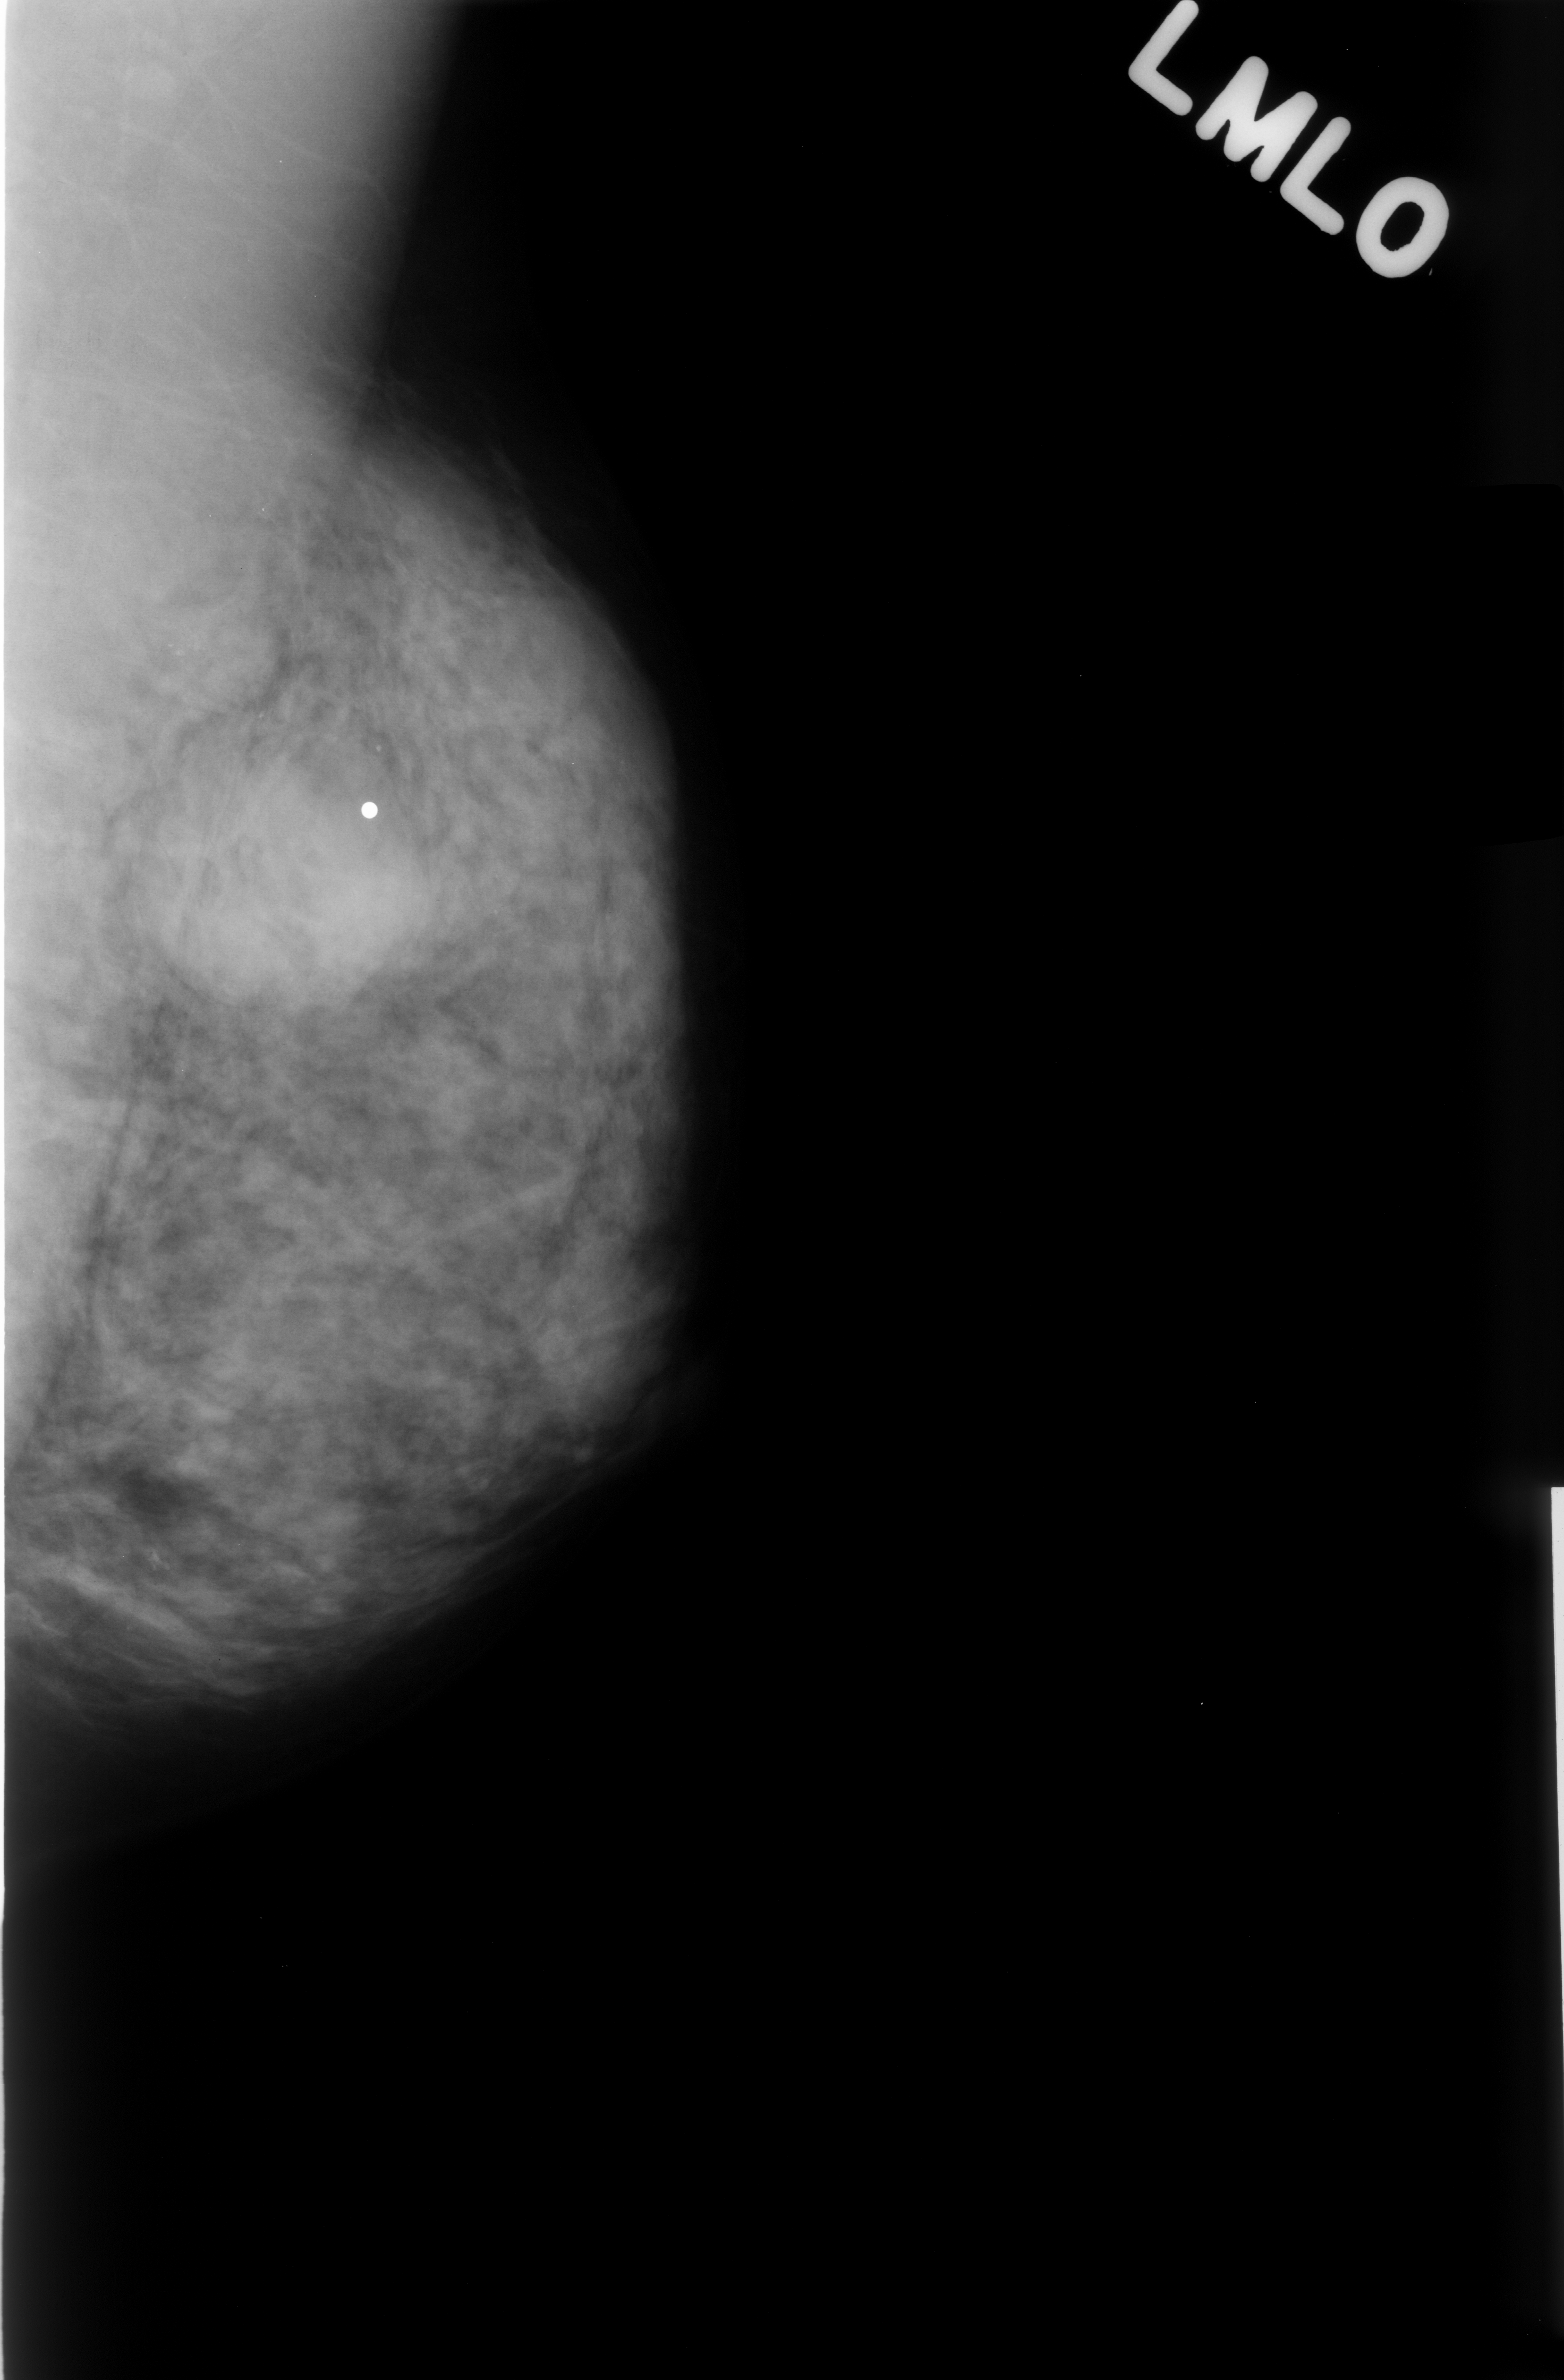
Mammogram (digitized film); left breast; MLO view; breast composition: heterogeneously dense (BI-RADS density category 3 of 4); 1564 × 2380 image matrix.
Expert-marked regions of interest on this film, with their recorded descriptors:
- calcifications, morphology dystrophic, distribution clustered; BI-RADS assessment category 3; pathology result (as recorded, not read from the image): benign: bounding box [x1, y1, x2, y2] px = [85, 1504, 205, 1612]